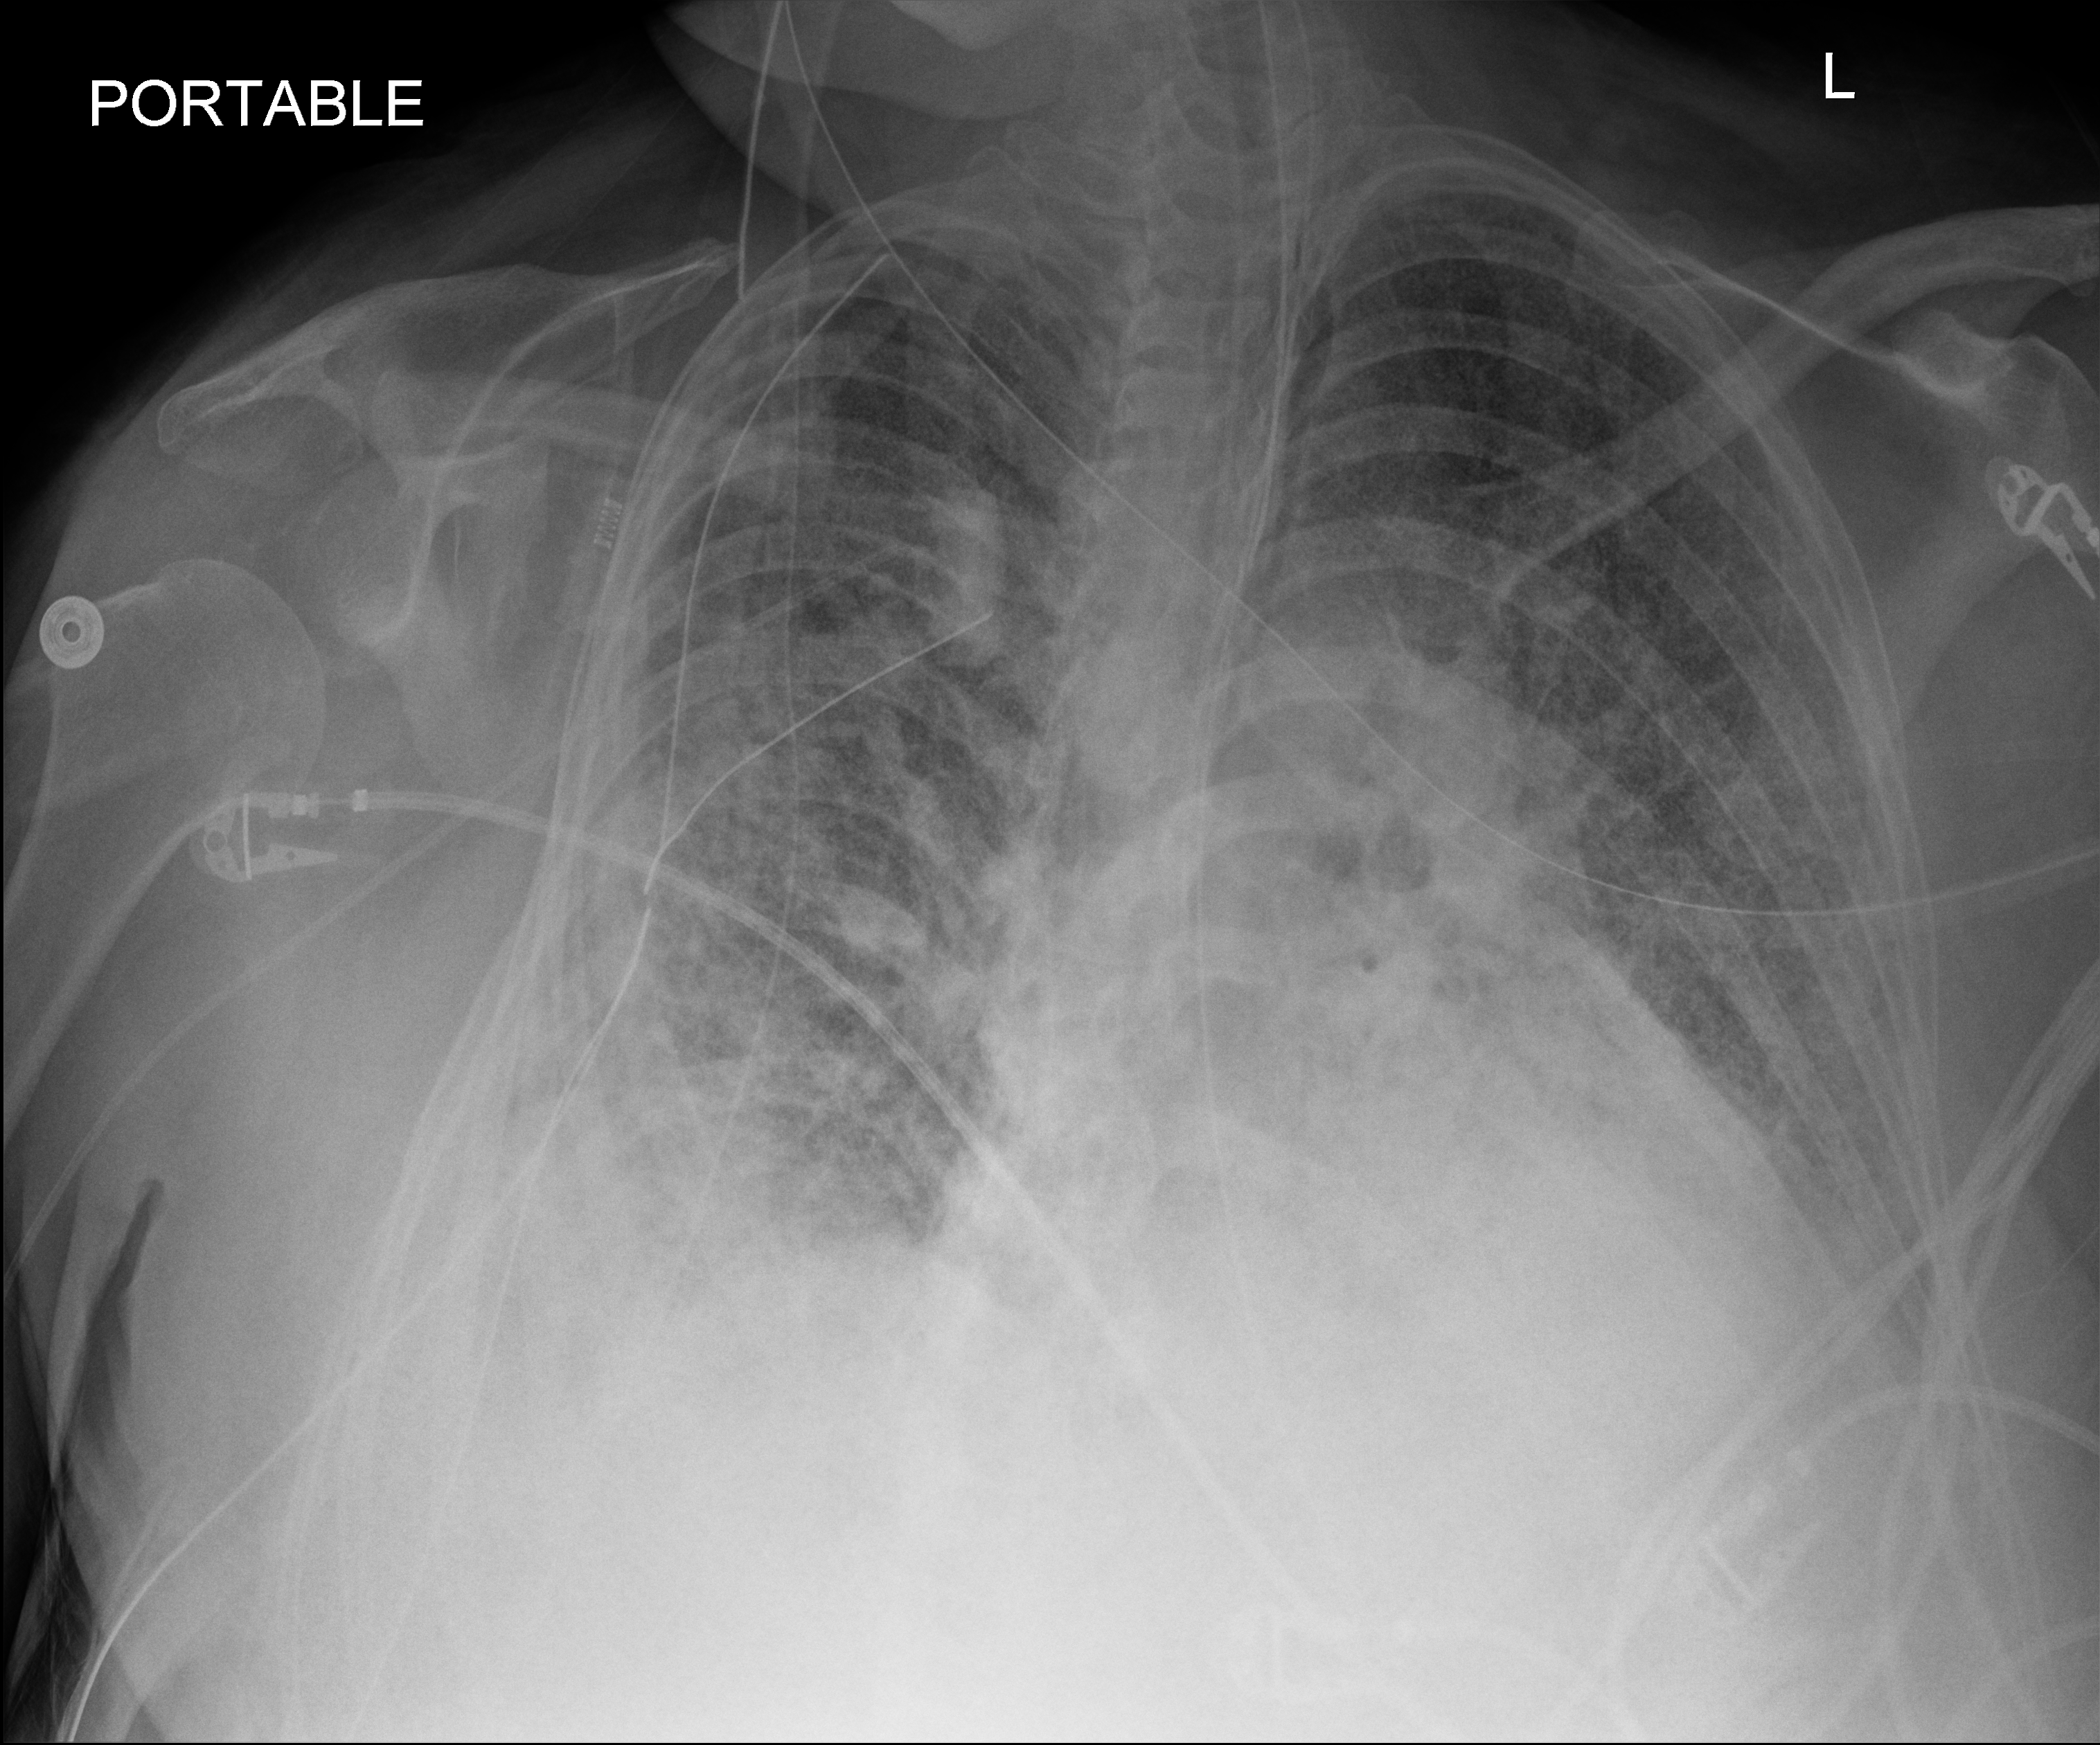
Bedside chest radiograph (digital radiography); anteroposterior (AP) projection. Adult patient hospitalised with COVID-19, age 18–59 years.
Admission-level facts for this patient (not findings on this image; timing relative to this image not recorded): diabetes (admission record): no.